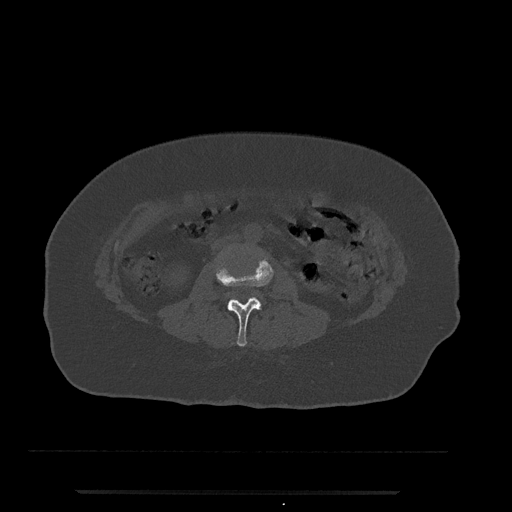
CT including the spine, one axial slice; position 14 of 797 along the scan axis; reconstruction kernel Br40s/3; bone window (W 1800 / L 400 HU); 0.5 mm slice thickness; 512 × 512 image matrix. Female patient, age 51 years. Case-level facts recorded for this patient, not image findings: primary cancer: neuro.
Outlined on this slice (semi-automatic segmentation, software-assisted and operator-edited):
- L2 vertebra: bounding box (x1, y1, x2, y2) in pixels: (216, 256, 274, 347)